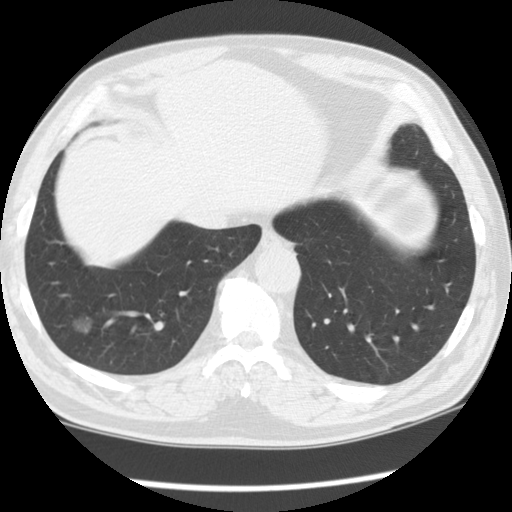
Axial slice from a low-dose chest CT screening exam, baseline annual screen, lung window (W 1500 / L -600 HU), standard (soft-tissue) reconstruction kernel (STANDARD), slice 91 of 122 in the series. Male, age 62 years at enrolment. Former smoker at enrolment.
- Lesion marked by an expert reader, bounding box [x1, y1, x2, y2] px = [52, 298, 112, 358].
- Reader record for this screening exam (exam-level; its link to the box is not recorded): non-calcified nodule or mass ≥4 mm, right lower lobe, 13 × 11 mm, smooth margins, ground glass attenuation.
- Official screen result: positive, change unspecified: nodule(s) >= 4 mm or enlarging nodule(s), mass(es), or other non-specific abnormalities suspicious for lung cancer.
- Lung cancer was diagnosed 874 days after this screen (after the second annual screen): bronchiolo-alveolar carcinoma, non-mucinous, right lower lobe, well differentiated (G1), stage IA (AJCC 6th edition), 14 mm at pathology.